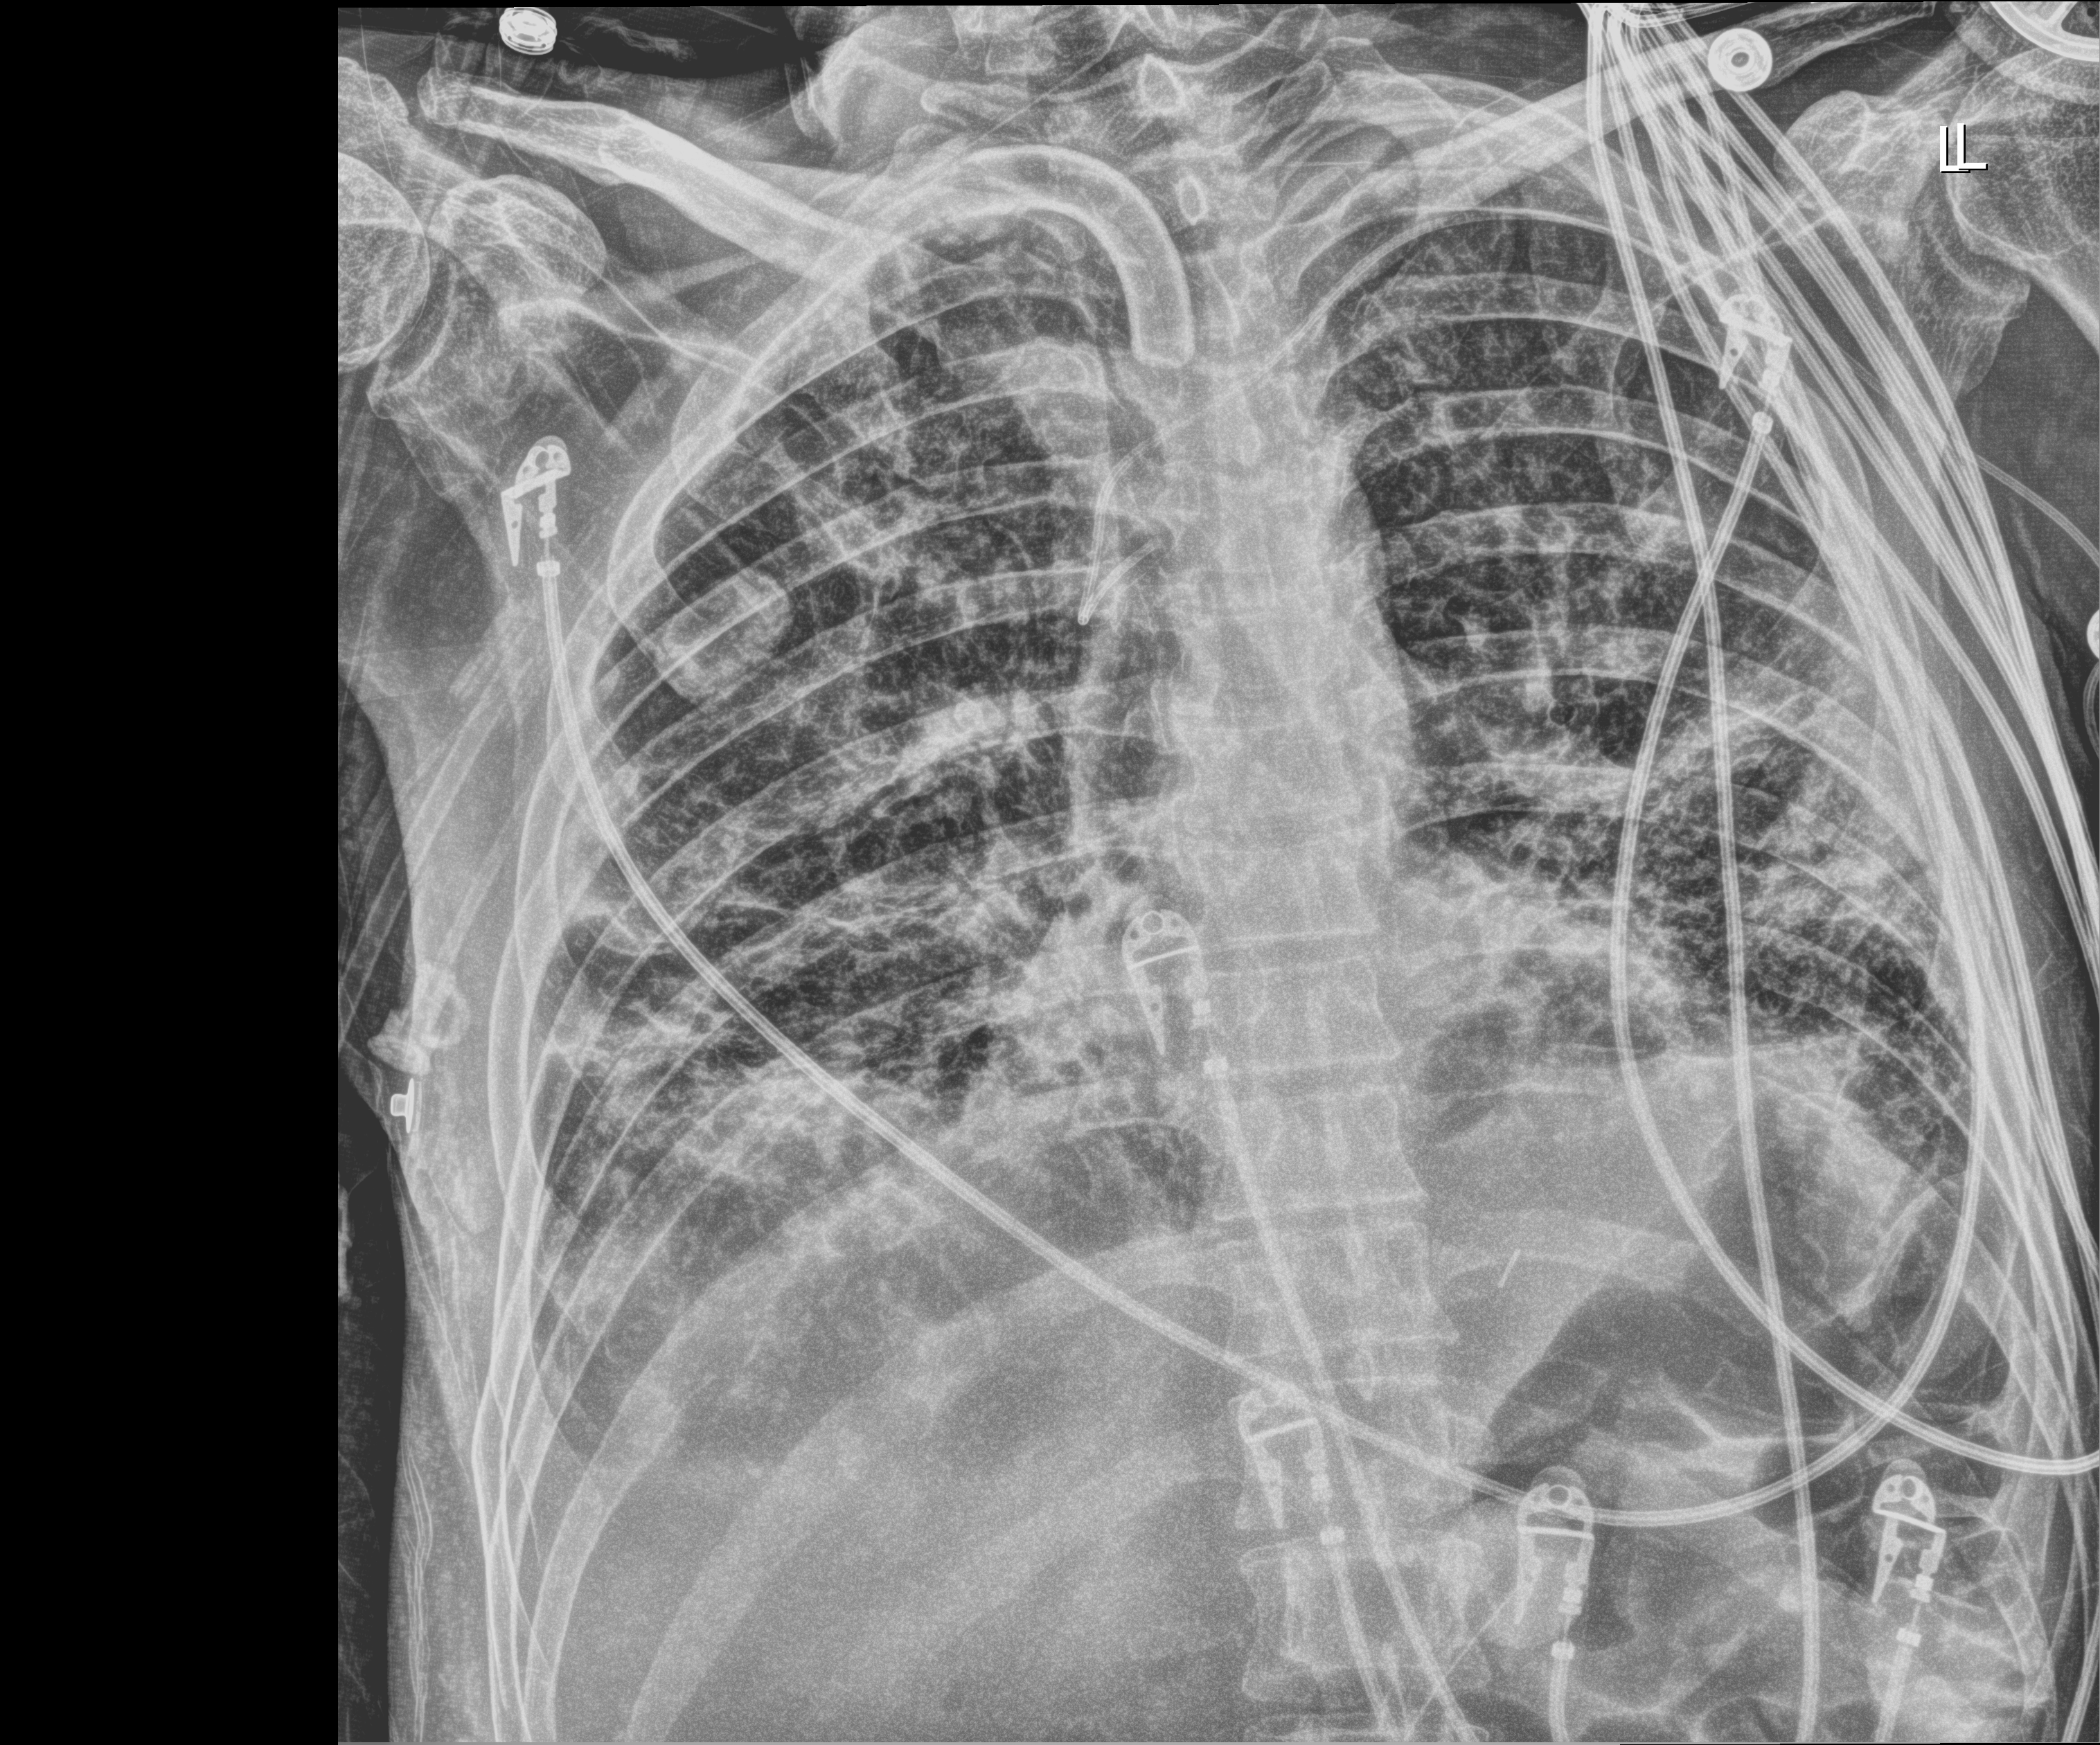
Chest radiograph (digital radiography); anteroposterior (AP) projection. Patient hospitalised with COVID-19; male, aged 18–59 years.
From the hospital-stay record, not from the radiograph (when in the stay this image was taken is not recorded): admitted to intensive care during this hospital stay: yes.